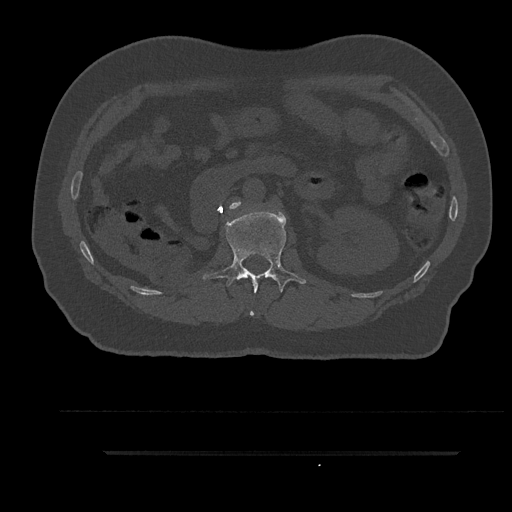
CT including the spine, one axial slice. Position 172 of 797 along the scan axis. 120 kVp. Bone window (W 1800 / L 400 HU). 0.5 mm slice thickness. 512 × 512 image matrix. Patient: male, 63 years. Case-level facts recorded for this patient, not image findings: primary cancer: renal.
Outlined on this slice (semi-automatically segmented with operator editing):
- L1 vertebra: bounding box [x1, y1, x2, y2] px = [203, 208, 306, 316]
- L2 vertebra: [229, 202, 241, 209]